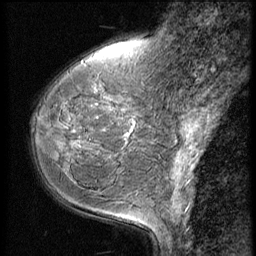
Breast MRI (dynamic contrast-enhanced), one sagittal slice. Position 18 of 56 along the scan axis. 3 images stored at this slice position (order not interpretable as contrast timing). 1.5 T. TE 4.2 ms, TR 9 ms. 2.5 mm slice thickness. 256 × 256 image matrix, field of view 180 × 180 mm. Patient: female, 49 years. From the clinical record (not read from this slice): setting: breast cancer imaged before/during neoadjuvant chemotherapy; receptor status: HER2-positive.
Structures marked on this image (semi-automatically segmented with operator editing):
- analysis volume of interest (the breast-tissue region the enhancement analysis was run in; not a lesion): bounding box (x1, y1, x2, y2) in pixels: (30, 74, 148, 198)
- tumour enhancement mask (voxels above the 140 % enhancement threshold inside the analysis volume of interest): (131, 130, 133, 133)